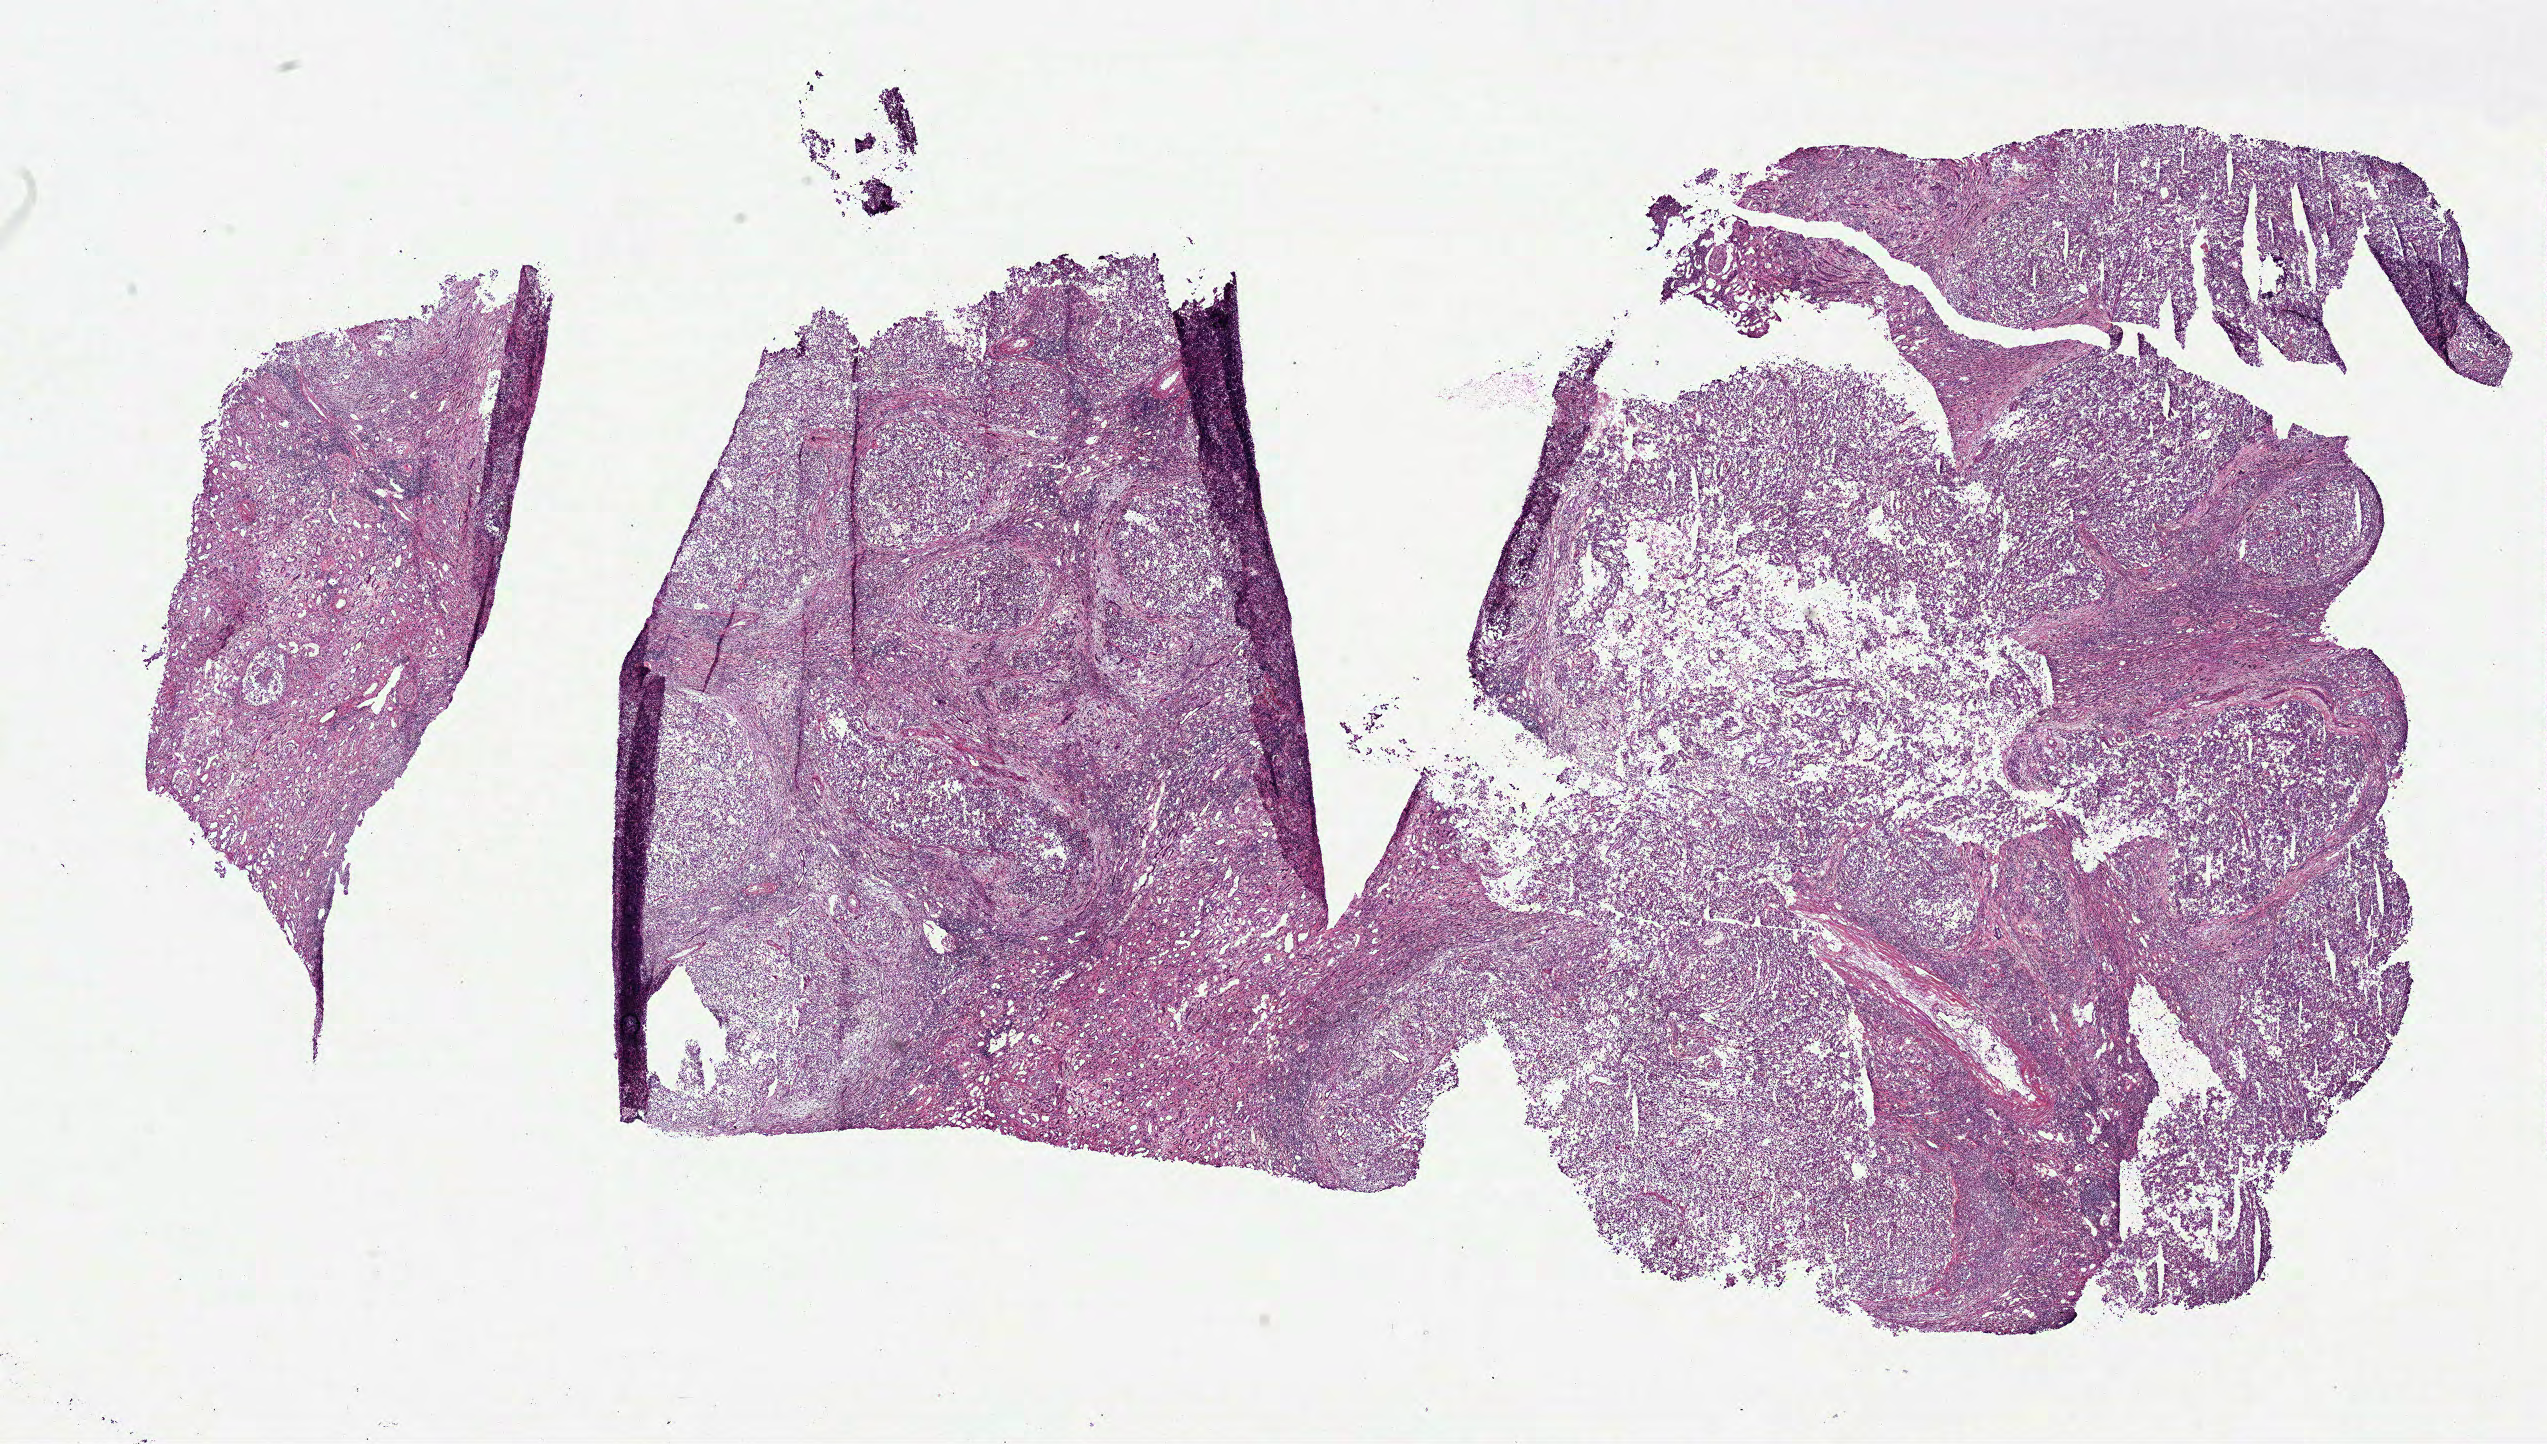
Hematoxylin and eosin (H&E) stained whole-slide image, whole scanned area (about 20.5 x 11.6 mm, acquisition: 40x scan) shown as a low-resolution overview; frozen section from the bottom of the tissue portion; sample: primary tumour, kidney. Patient: male, age at initial diagnosis 63 years. Pathologist review of this section (percent, as recorded): tumour cells 66%, tumour nuclei 75%, normal cells 18%, stromal cells 15%, necrosis 1%.
- TNM: T3b N1 M1
- pathologic diagnosis: Papillary adenocarcinoma, NOS
- AJCC pathologic stage: IV